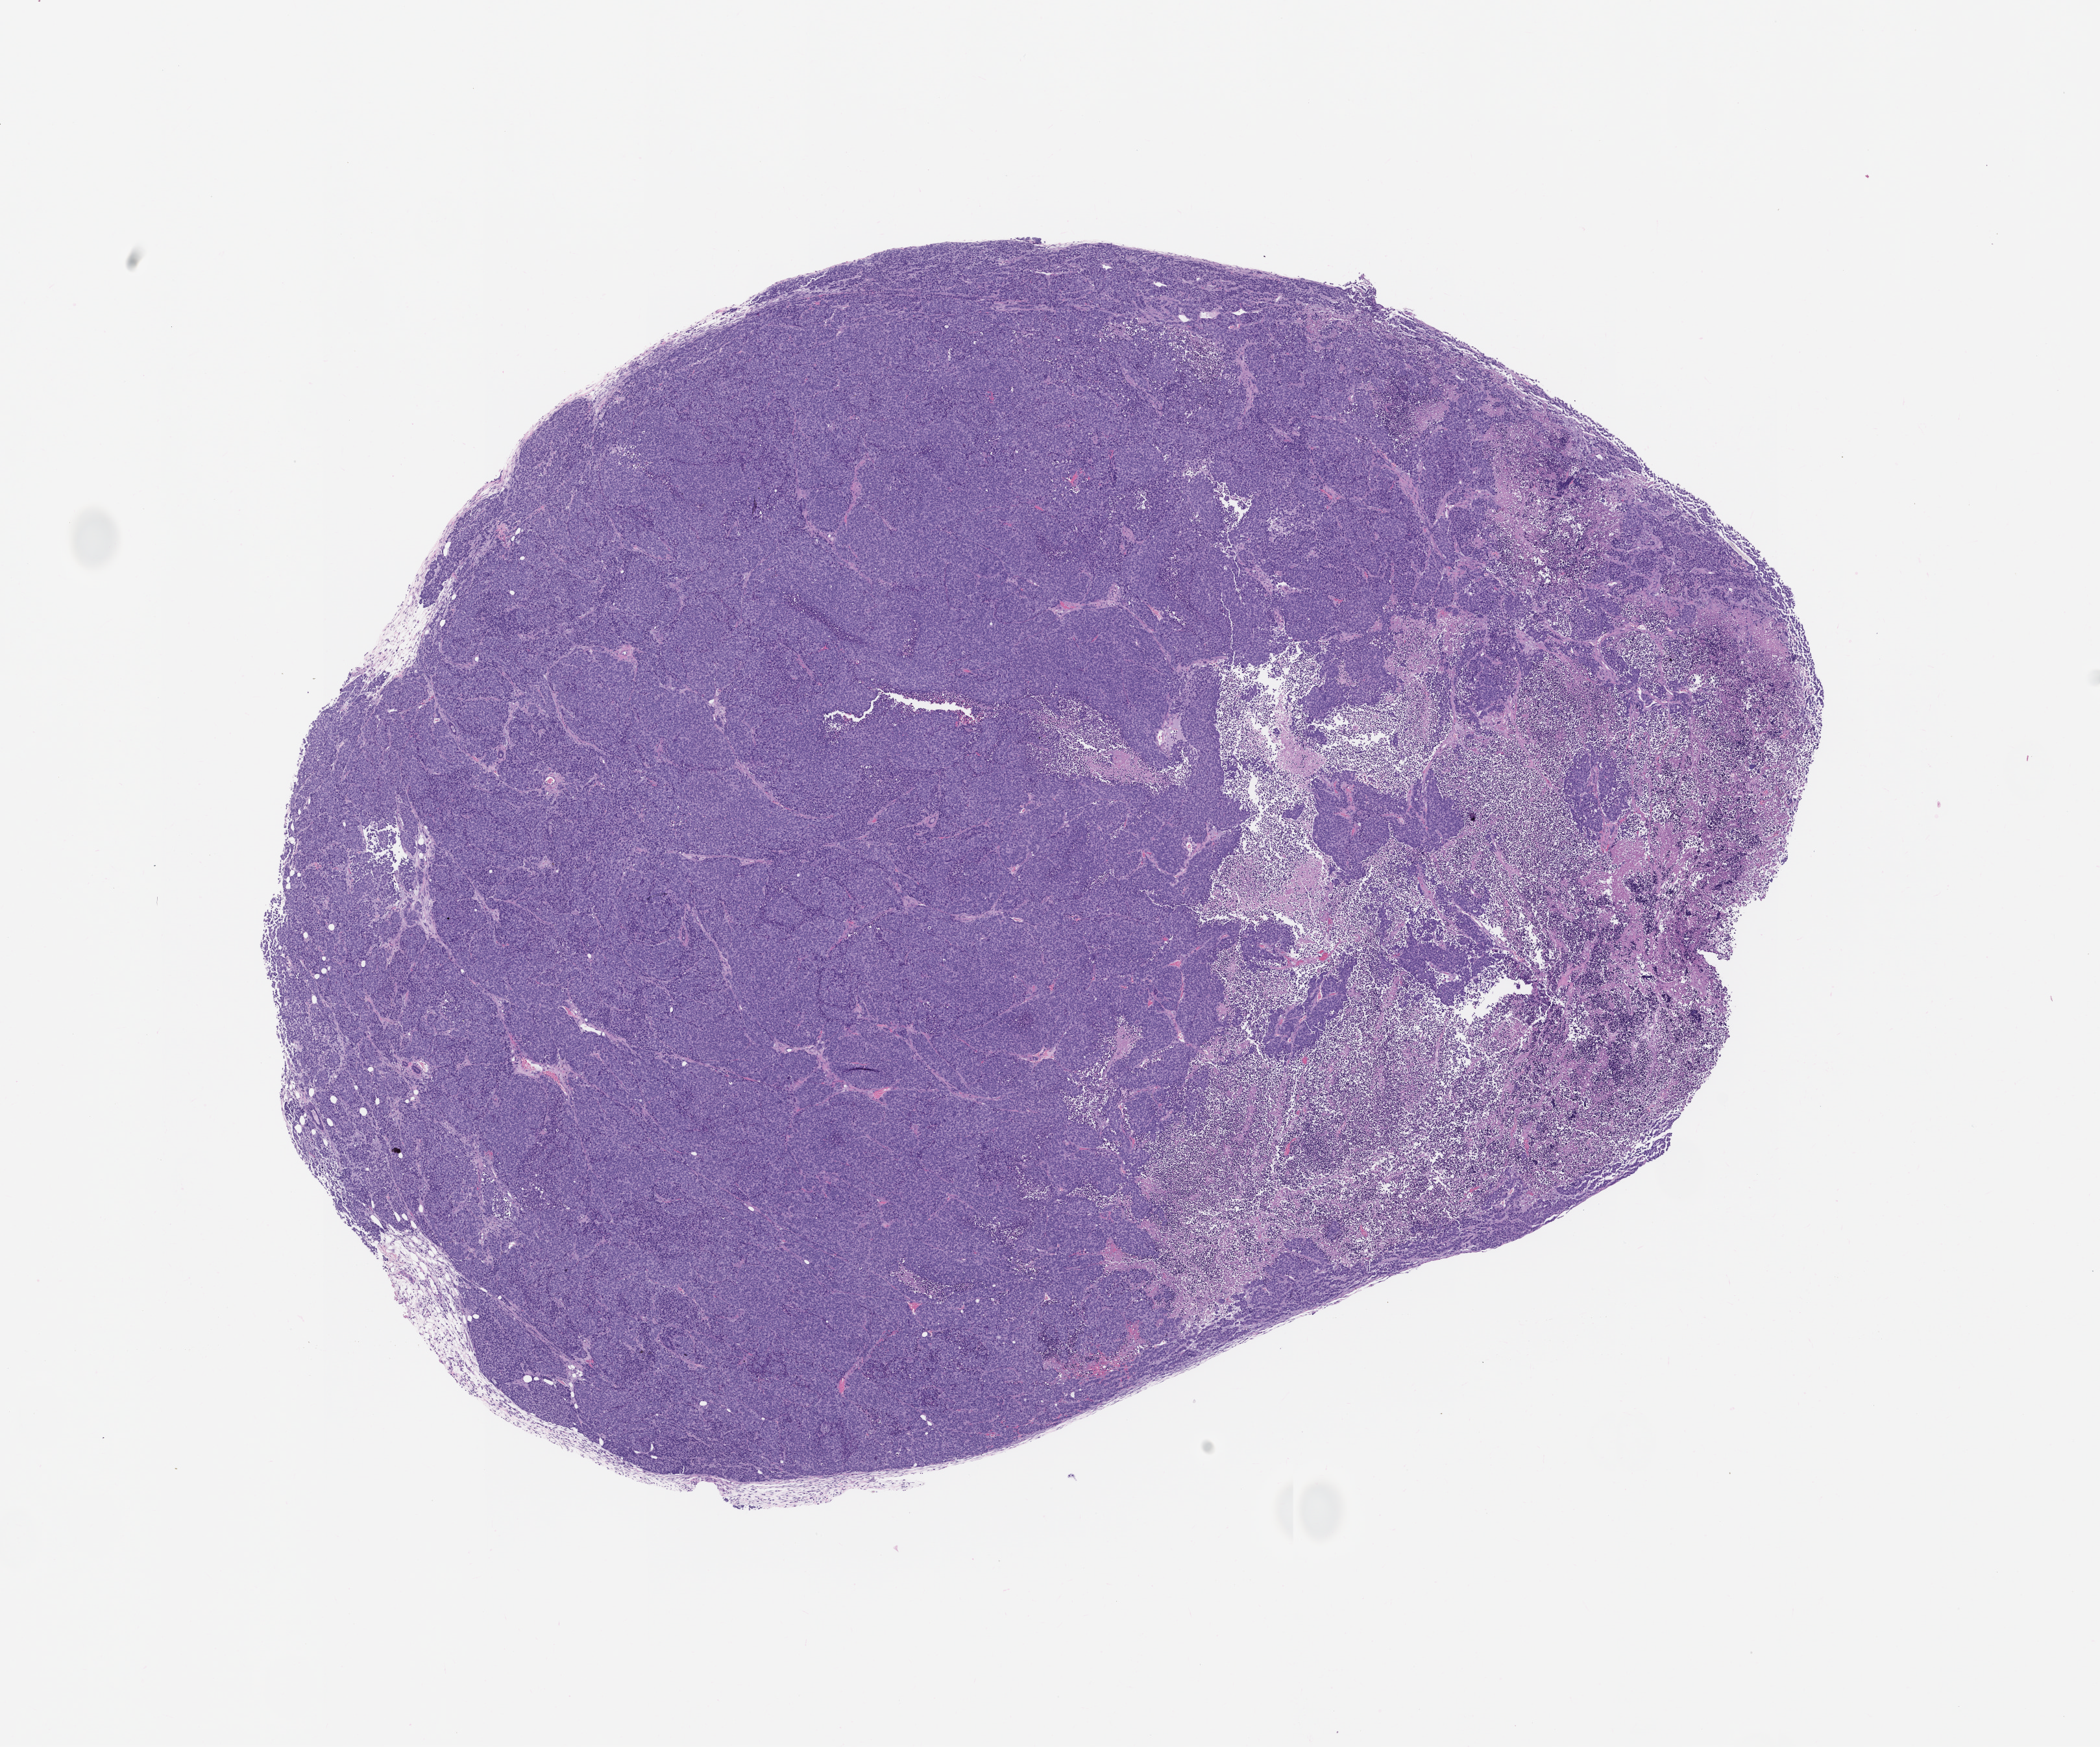
Whole-slide image, haematoxylin and eosin: patient-derived xenograft (human tumor grown in a mouse), passage 1 — shown as a low-resolution overview of the whole scanned area (about 13.0 x 10.8 mm); FFPE section; tumor site category: bladder.
Originating patient diagnosis: Bladder Small Cell Neuroendocrine Carcinoma.